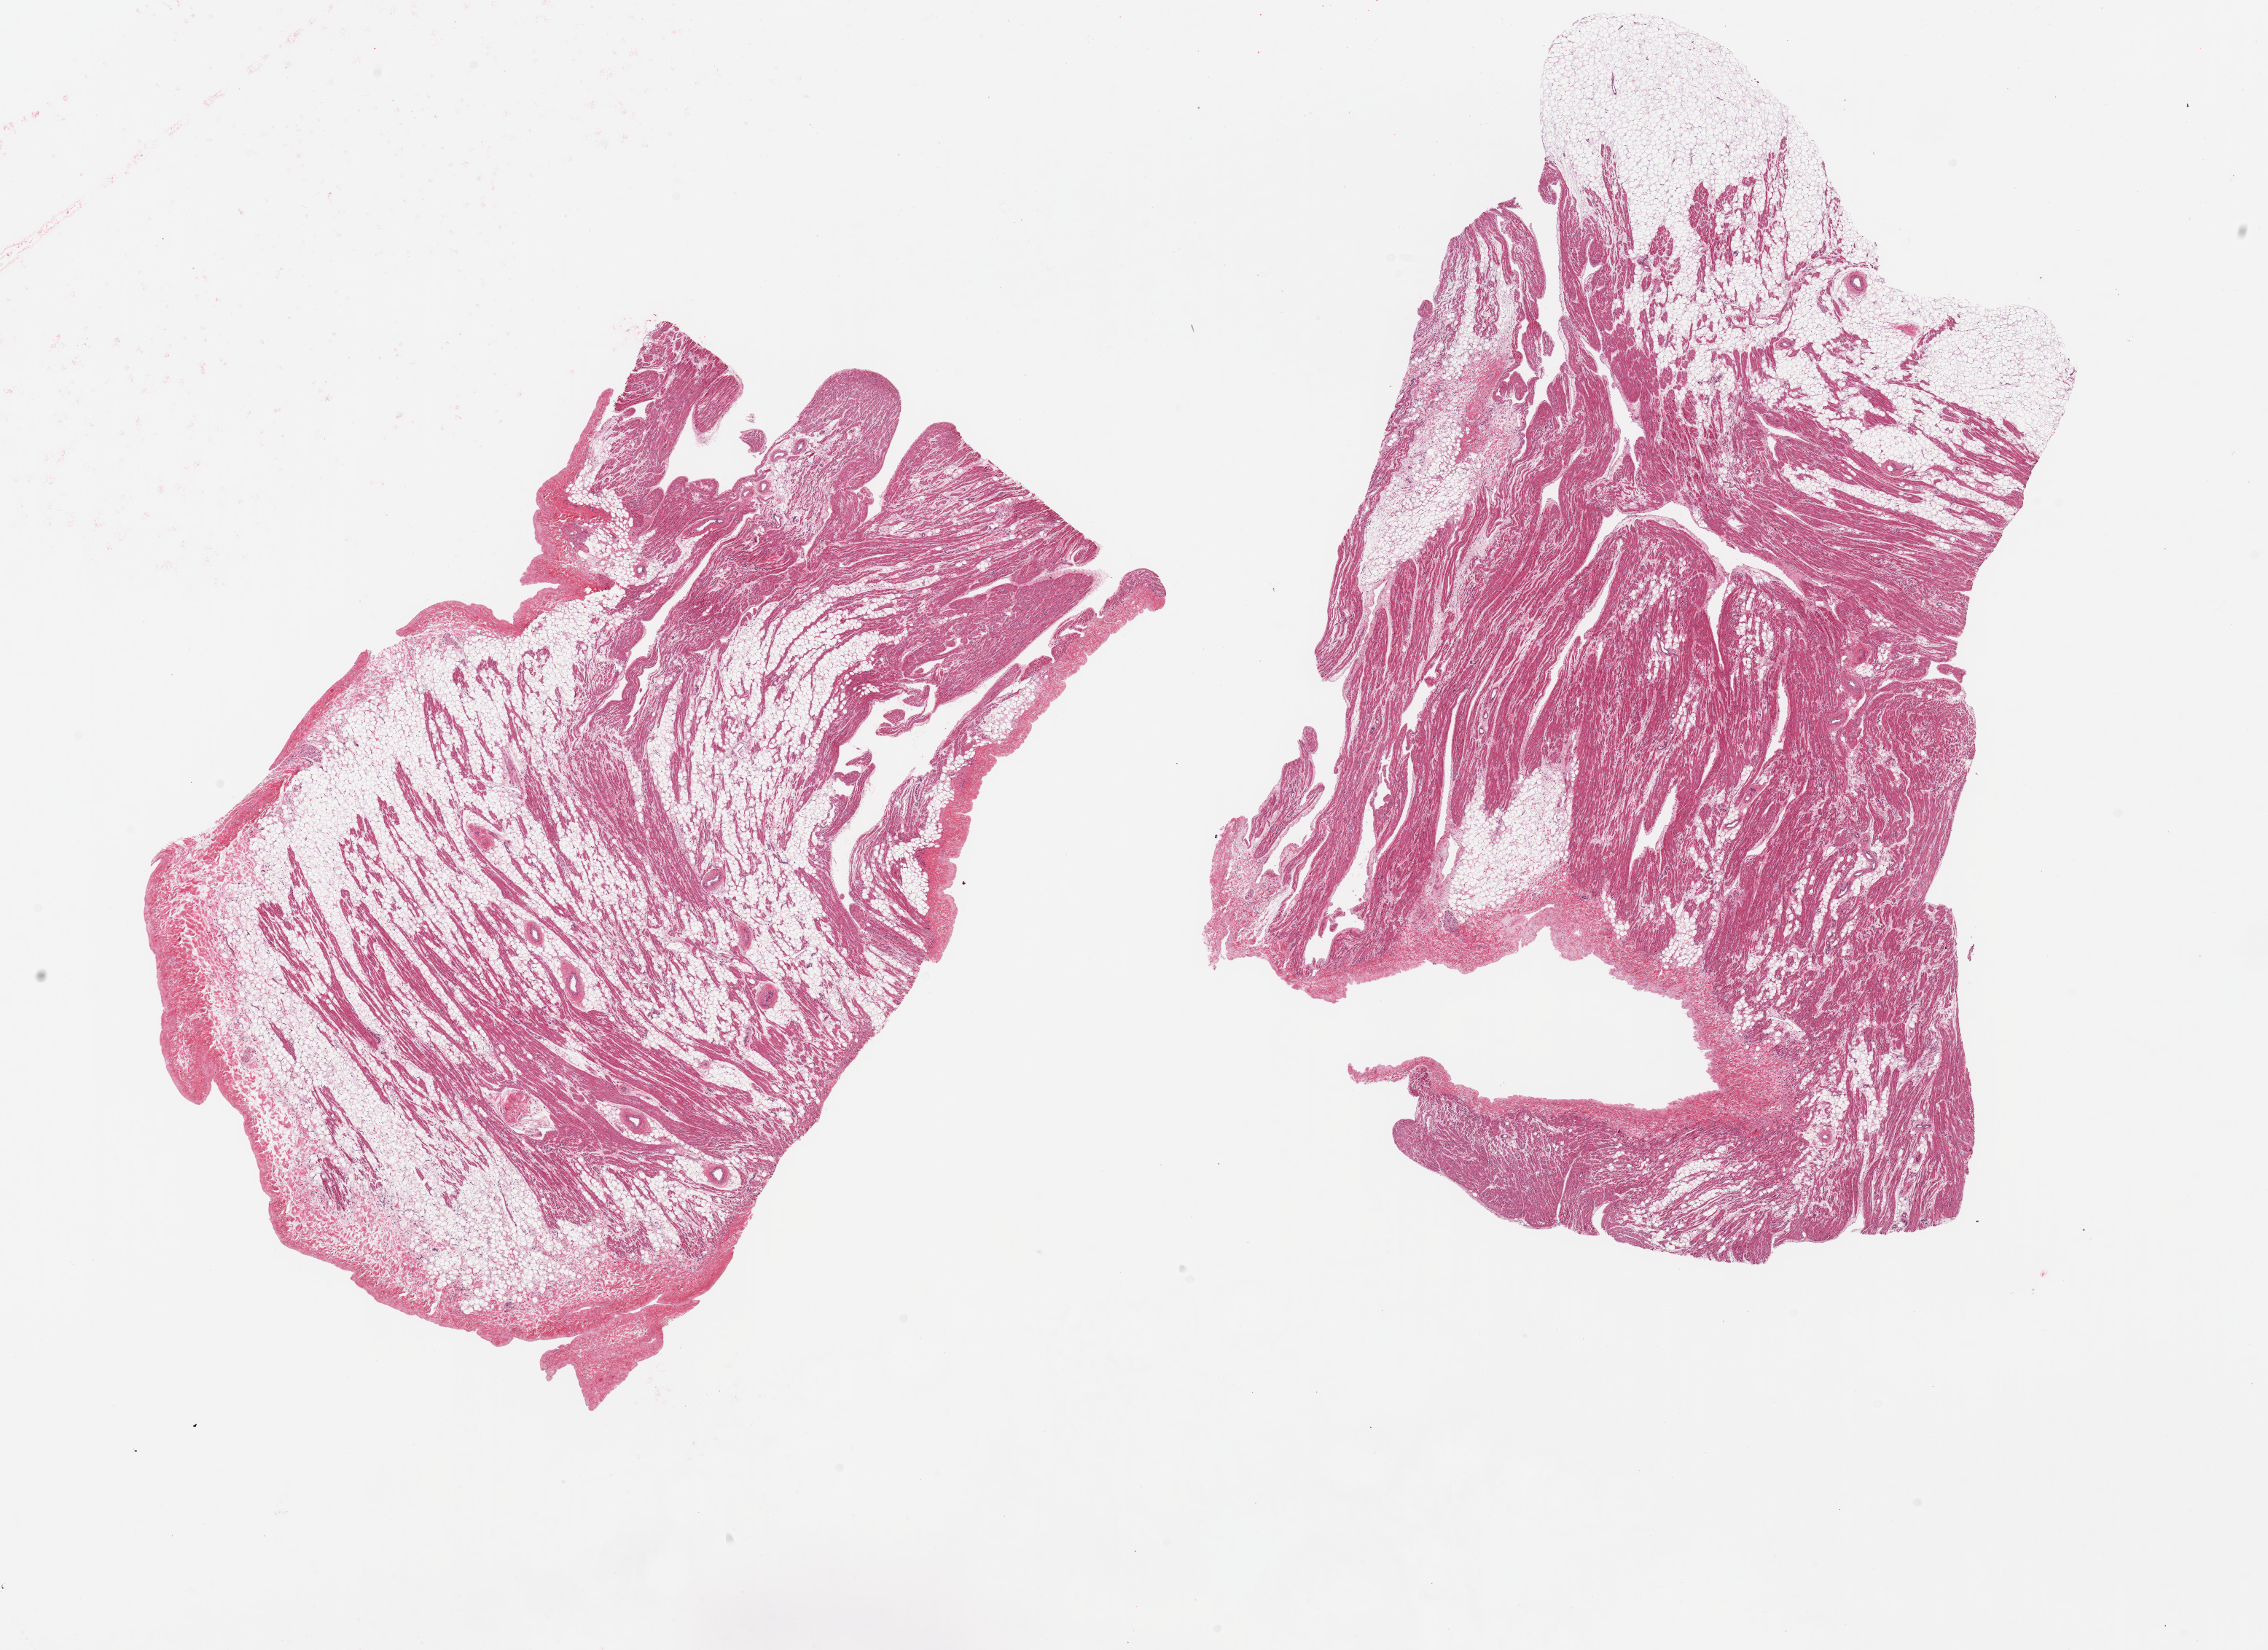
Hematoxylin and eosin (H&E) whole-slide image — whole scanned area (about 24.6 x 17.9 mm, from a 20x scan) shown as a low-resolution overview; PAXgene-fixed, paraffin-embedded tissue; target tissue: auricular appendage; tissue donor sample. Donor sex: female.
• review note (as recorded): 2 pieces; from 30-60% fat